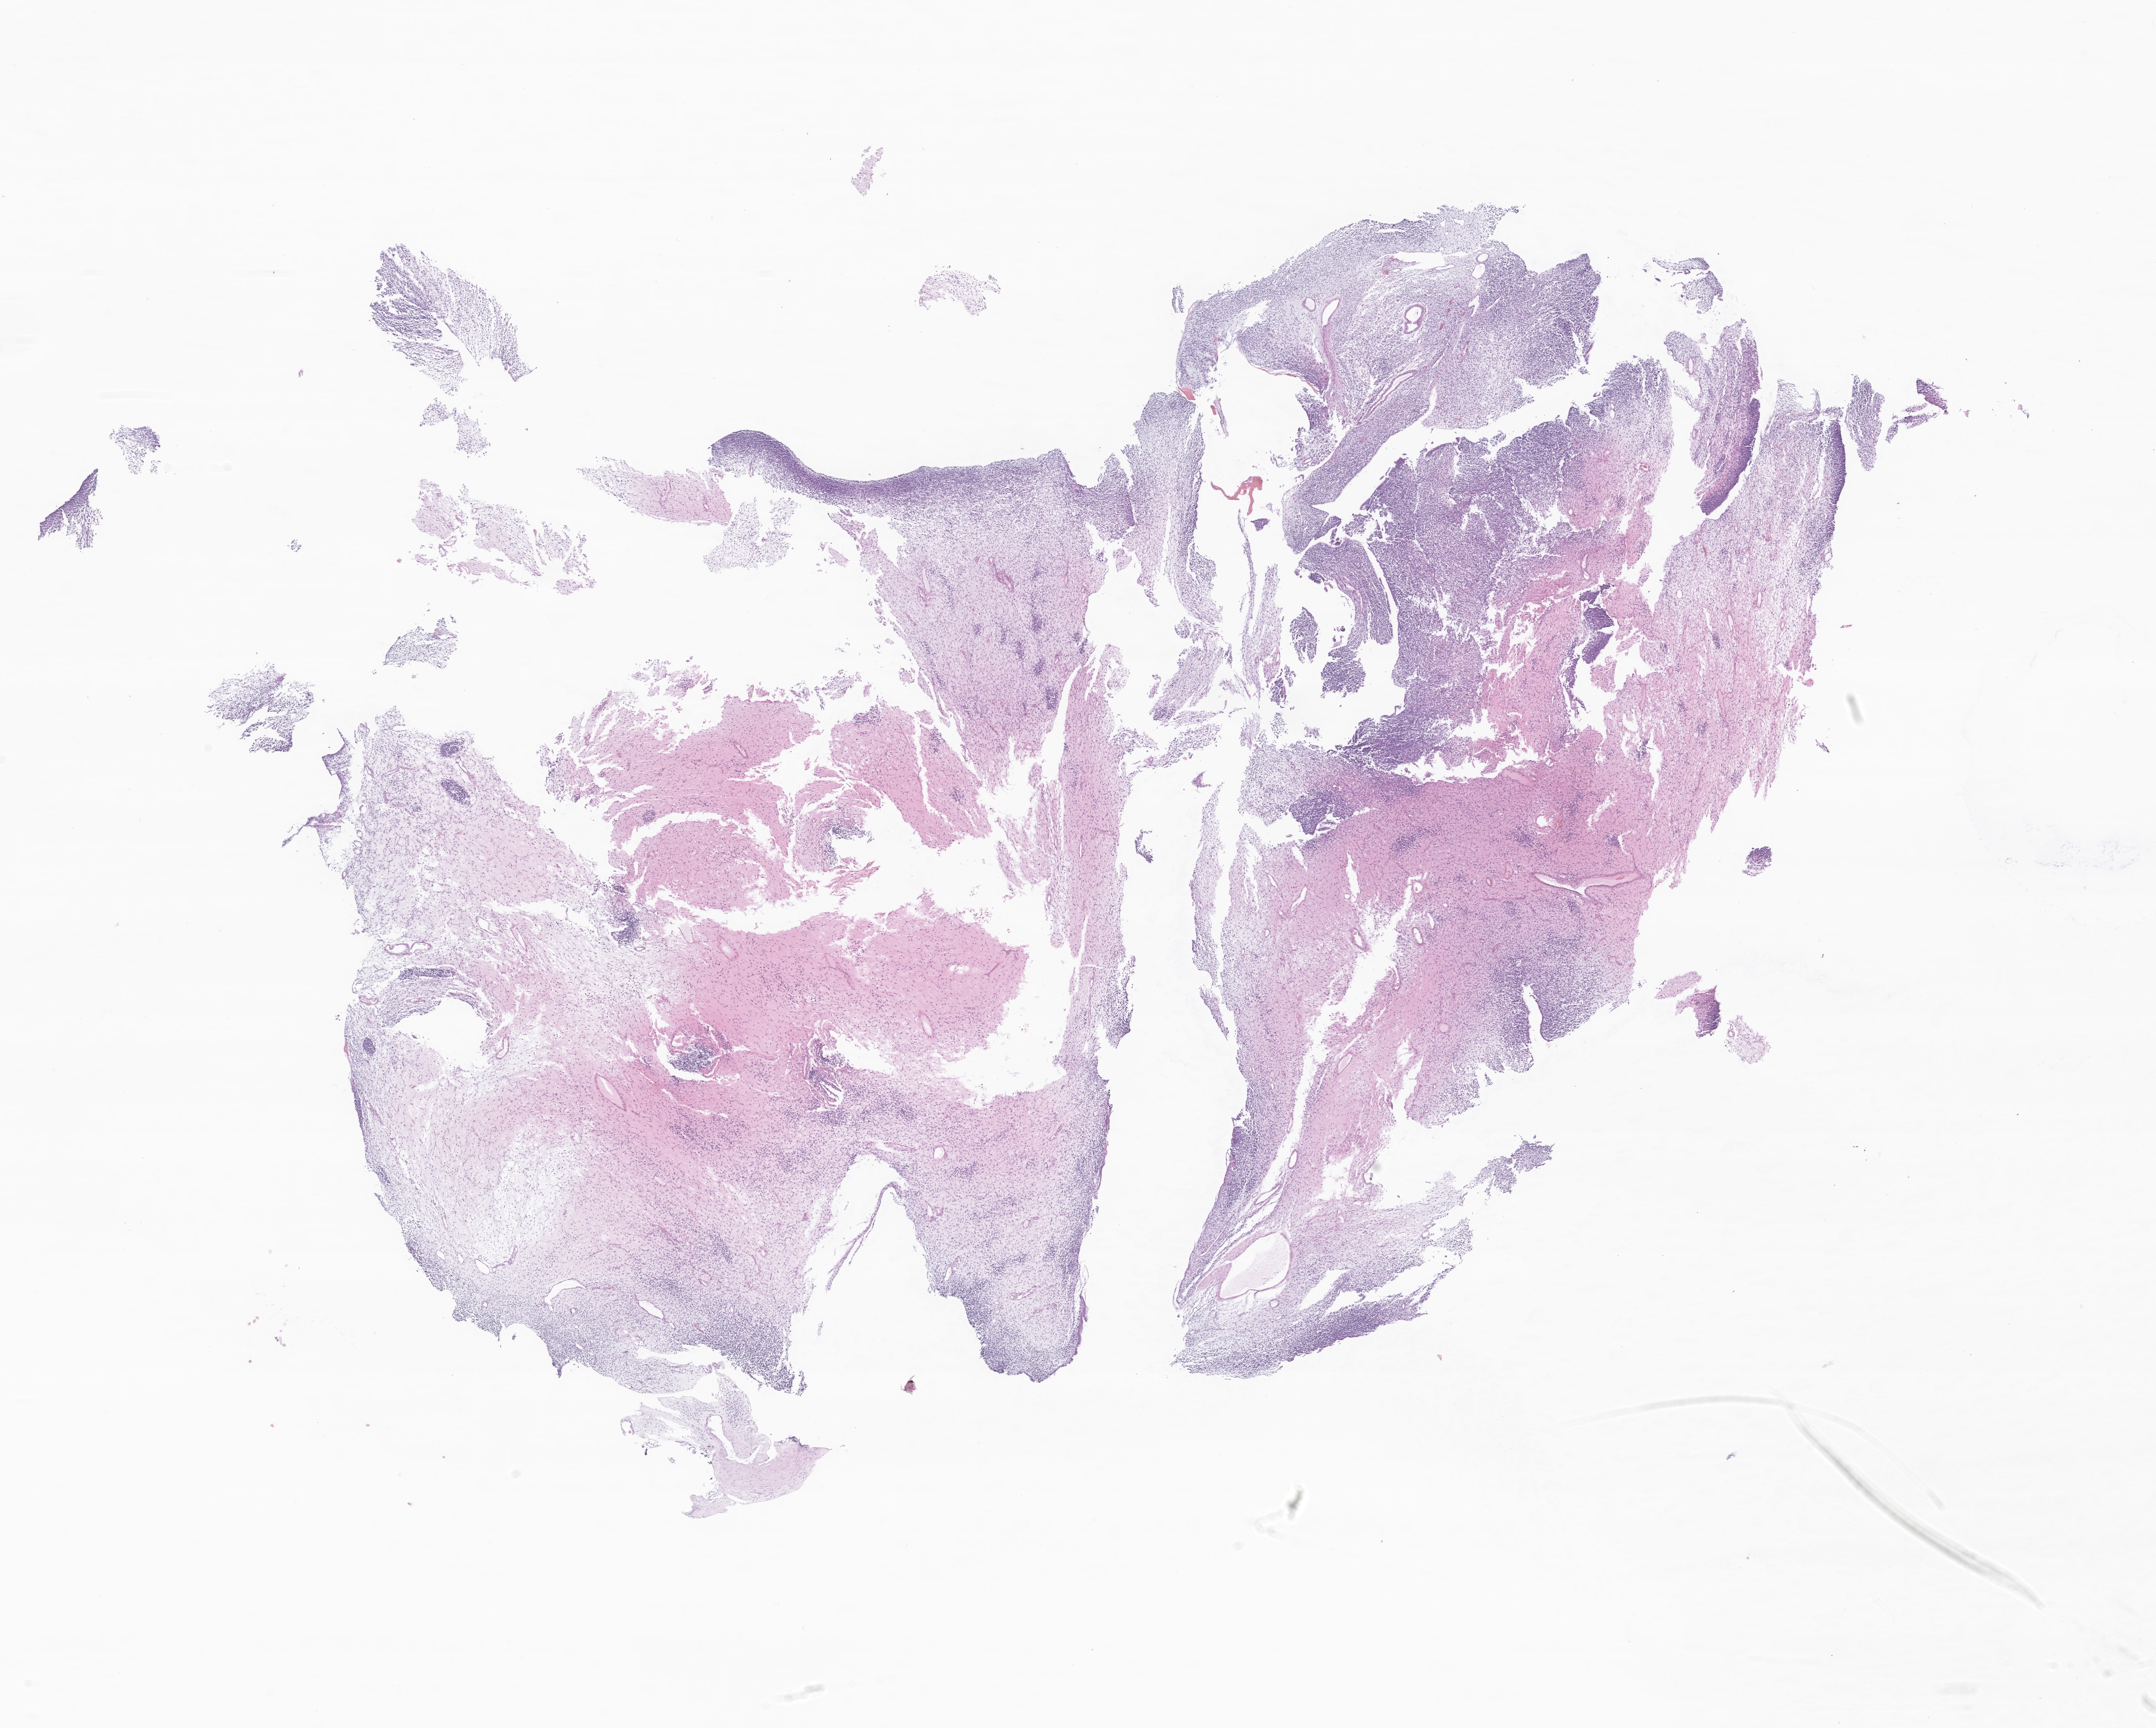
Whole-slide image, hematoxylin and eosin (H&E) stain of tumor tissue from the intrahepatic bile duct — a low-resolution overview of the entire scanned area, about 19.4 x 15.5 mm. Formalin-fixed paraffin-embedded section. Patient male; age 68 months (5 years 8 months).
Diagnosis (ICD-O-3 morphology term): Rhabdomyosarcoma, NOS.